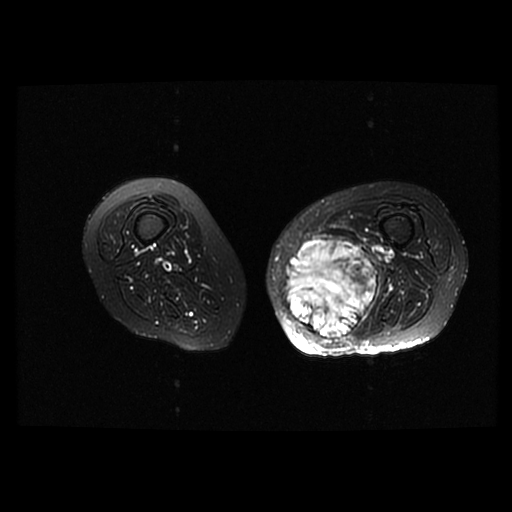
MRI of an extremity soft-tissue mass, one axial slice. Position 27 of 42 along the scan axis. T2-weighted fat-saturated. 512 × 512 image matrix, field of view 420 × 420 mm. Female patient. From the clinical record (not read from this slice): histological type: pleomorphic leiomyosarcoma; grade: high; site of the primary tumour: left thigh.
Outlined on this slice (manually delineated by an expert):
- gross tumour volume including surrounding oedema: bounding box [x1, y1, x2, y2] px = [280, 234, 380, 338]
- gross tumour volume (mass): [280, 237, 378, 338]